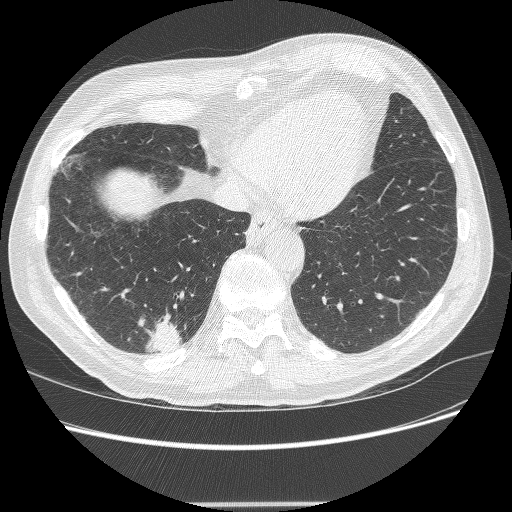
Chest CT (low-dose screening protocol), one axial image, second screening round (one year after baseline), lung window (W 1500 / L -600 HU), 1.25 mm slice thickness, 512 × 512 image matrix, field of view 372 × 372 mm. Male, age 71 years at enrolment.
• Expert reader's lesion annotation, bounding box <137,322,187,360> (left, top, right, bottom; pixels).
• The screening reader recorded 5 non-calcified nodules or masses ≥4 mm on this exam (right lower lobe, right lower lobe, right upper lobe, right upper lobe, right upper lobe); which of them this box marks is not recorded.
• Later outcome: lung cancer diagnosed 7 days after this screen — squamous cell carcinoma, NOS, right lower lobe, moderately differentiated (G2), stage IA (AJCC 6th edition), 27 mm at pathology.